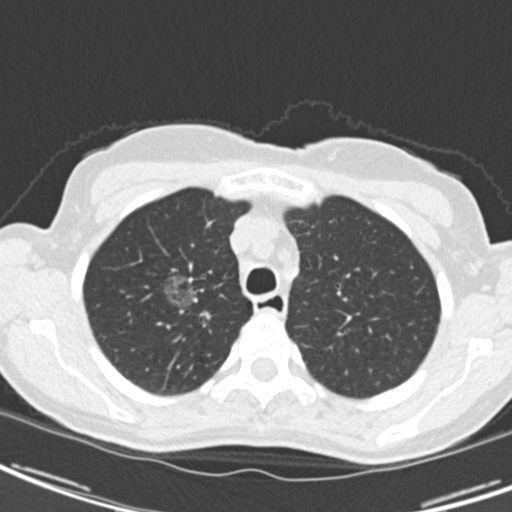
Low-dose screening chest CT, one axial slice. Slice 157 of 189 in the series (ordered by position). Reconstruction kernel B30f. 120 kVp. Lung window (W 1500 / L -600 HU). 512 × 512 image matrix, field of view 279 × 279 mm.
Outlined on this slice (manually delineated by an expert):
- lesion 1 (tumor, upper lobe of right lung): bounding box [x1, y1, x2, y2] px = [162, 273, 198, 309]